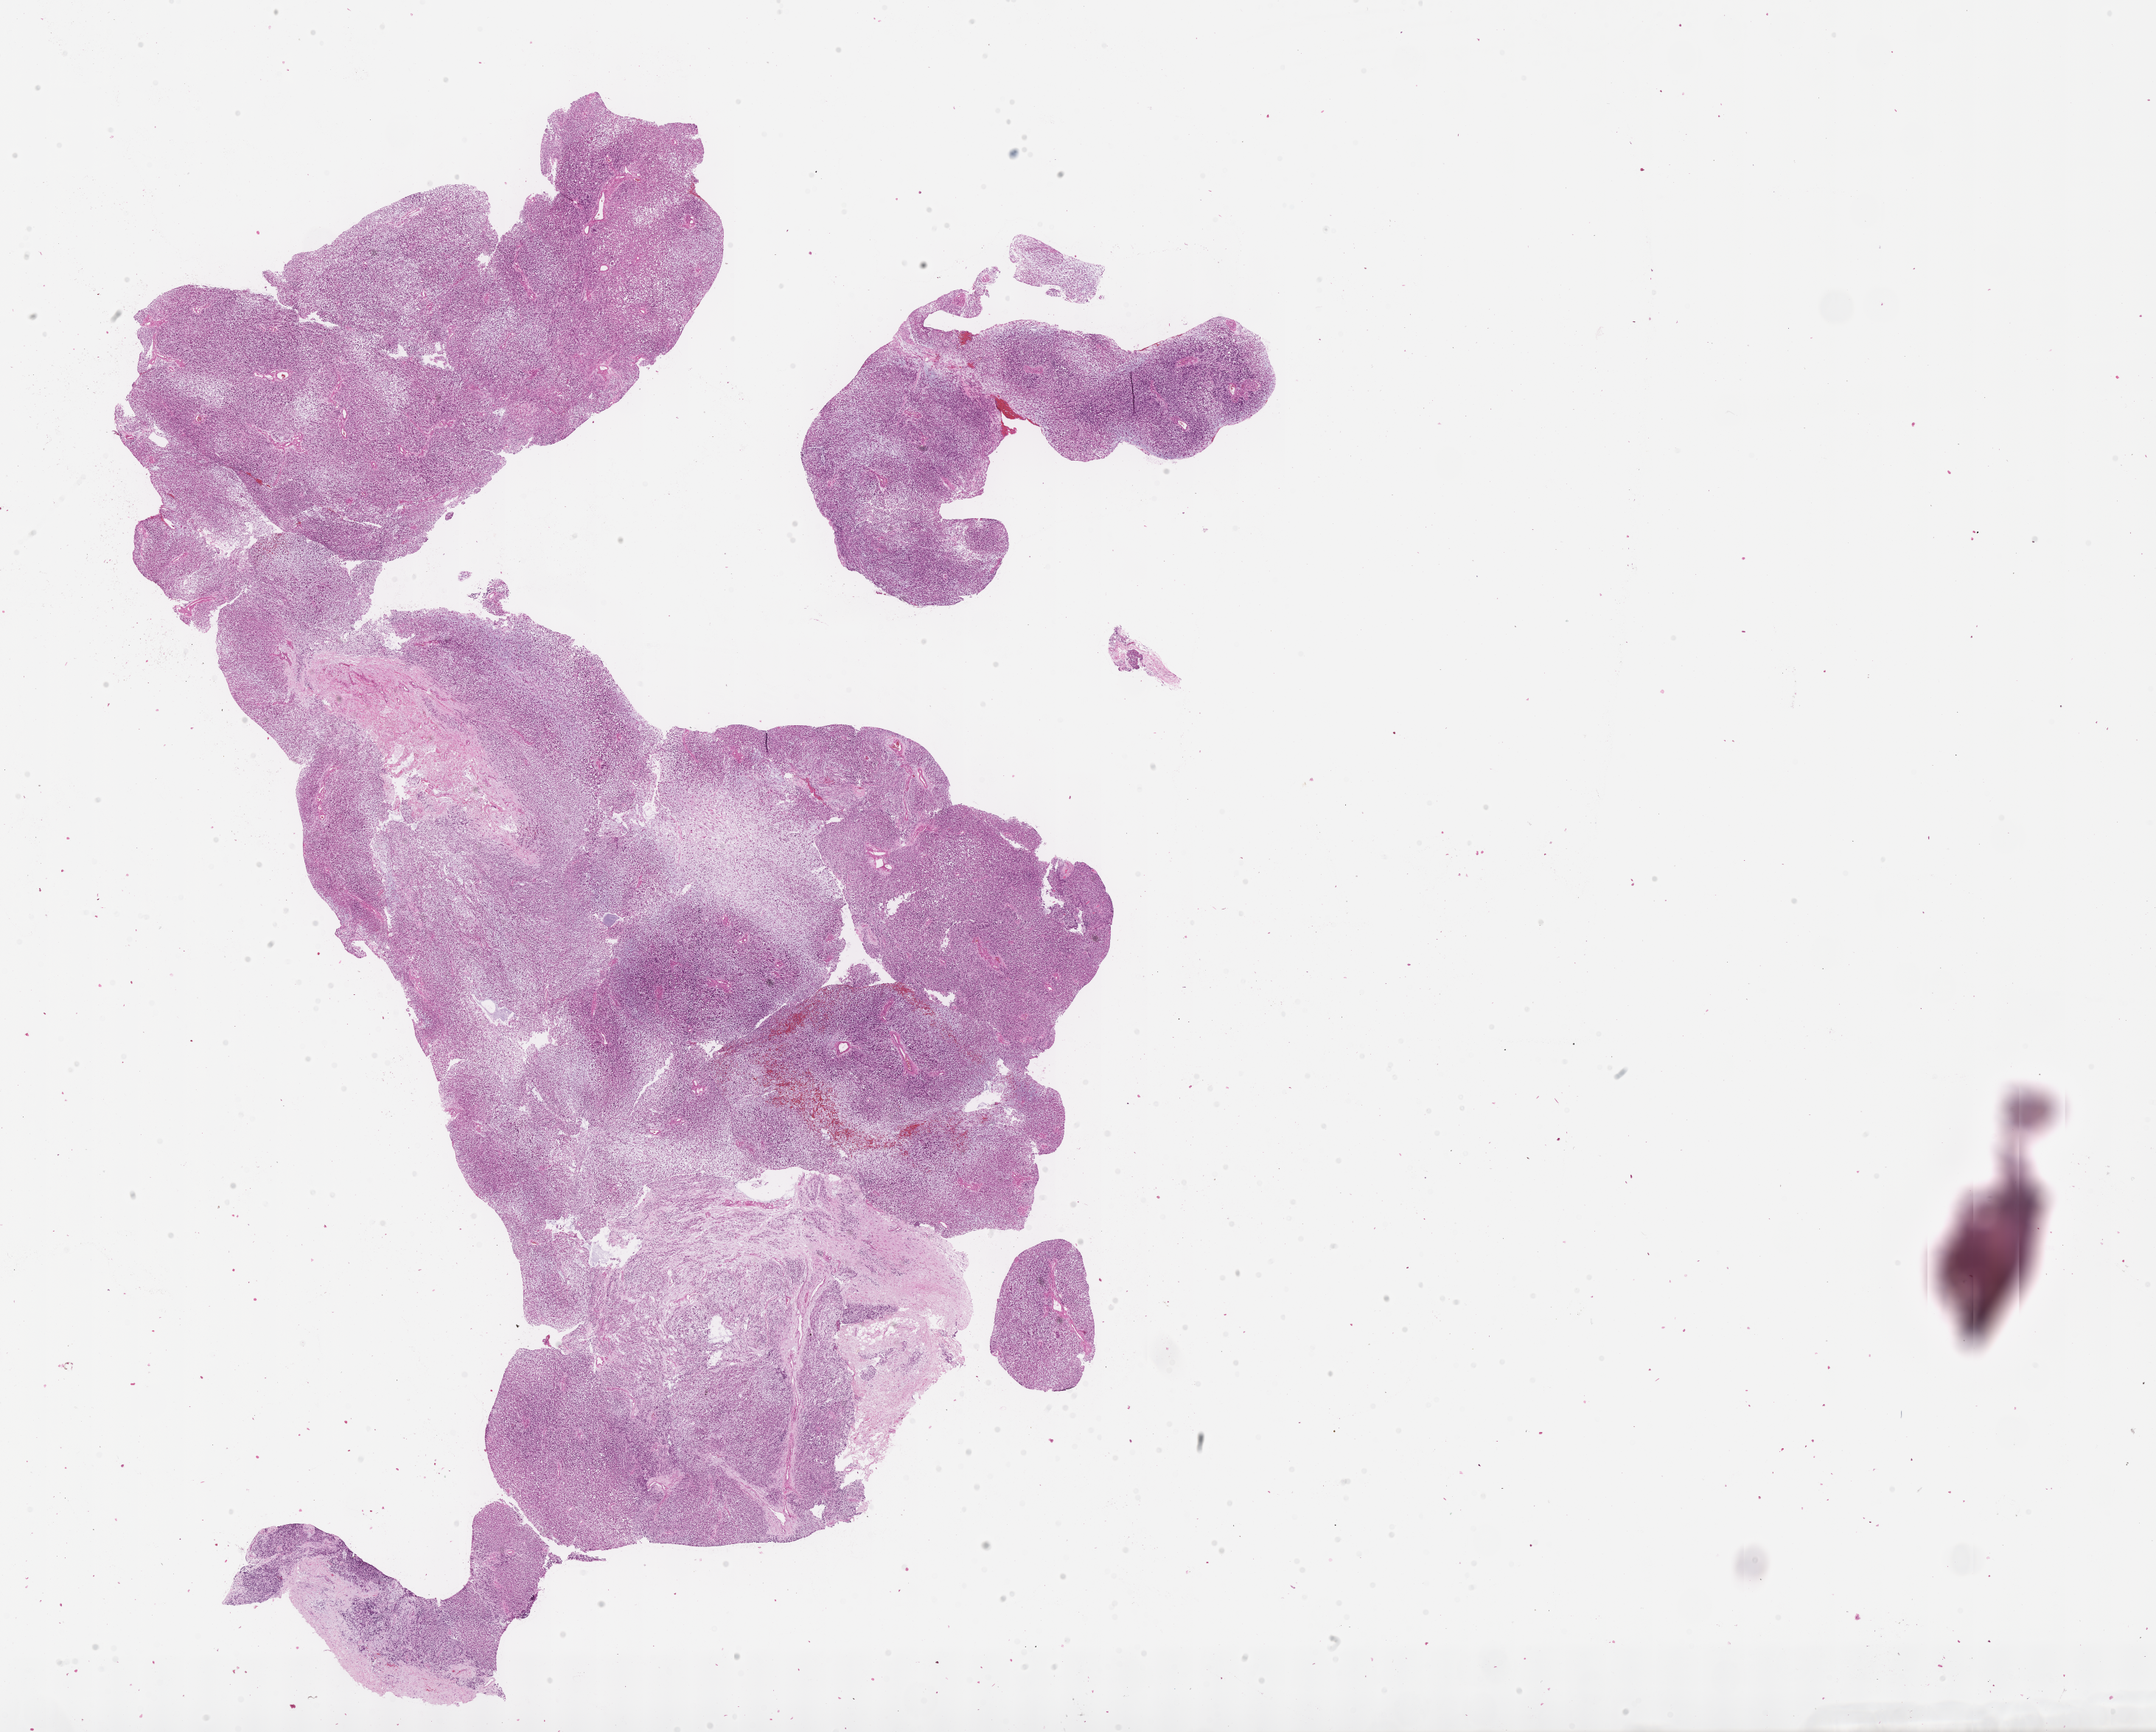
Digitized haematoxylin and eosin-stained section of tumor tissue, low-resolution overview of the scanned area, about 23.6 x 19.0 mm. Formalin-fixed, paraffin-embedded (FFPE) tissue. Sample anatomic site: eye, orbit-right. Male patient, age at diagnosis 9.3 years.
* metastatic status at presentation (as recorded): non-metastatic
* stage (as recorded): 1
* diagnosis: rhabdomyosarcoma; histological classification: embryonal rhabdomyosarcoma